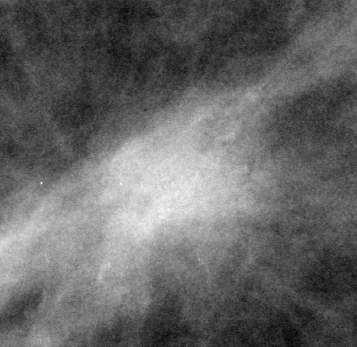
Crop from a digitized film mammogram around one marked abnormality; right breast; MLO view; BI-RADS breast density category 2 (scale 1–4).
Mass, shape irregular, margins spiculated; BI-RADS assessment category 5; pathology (as recorded): malignant.